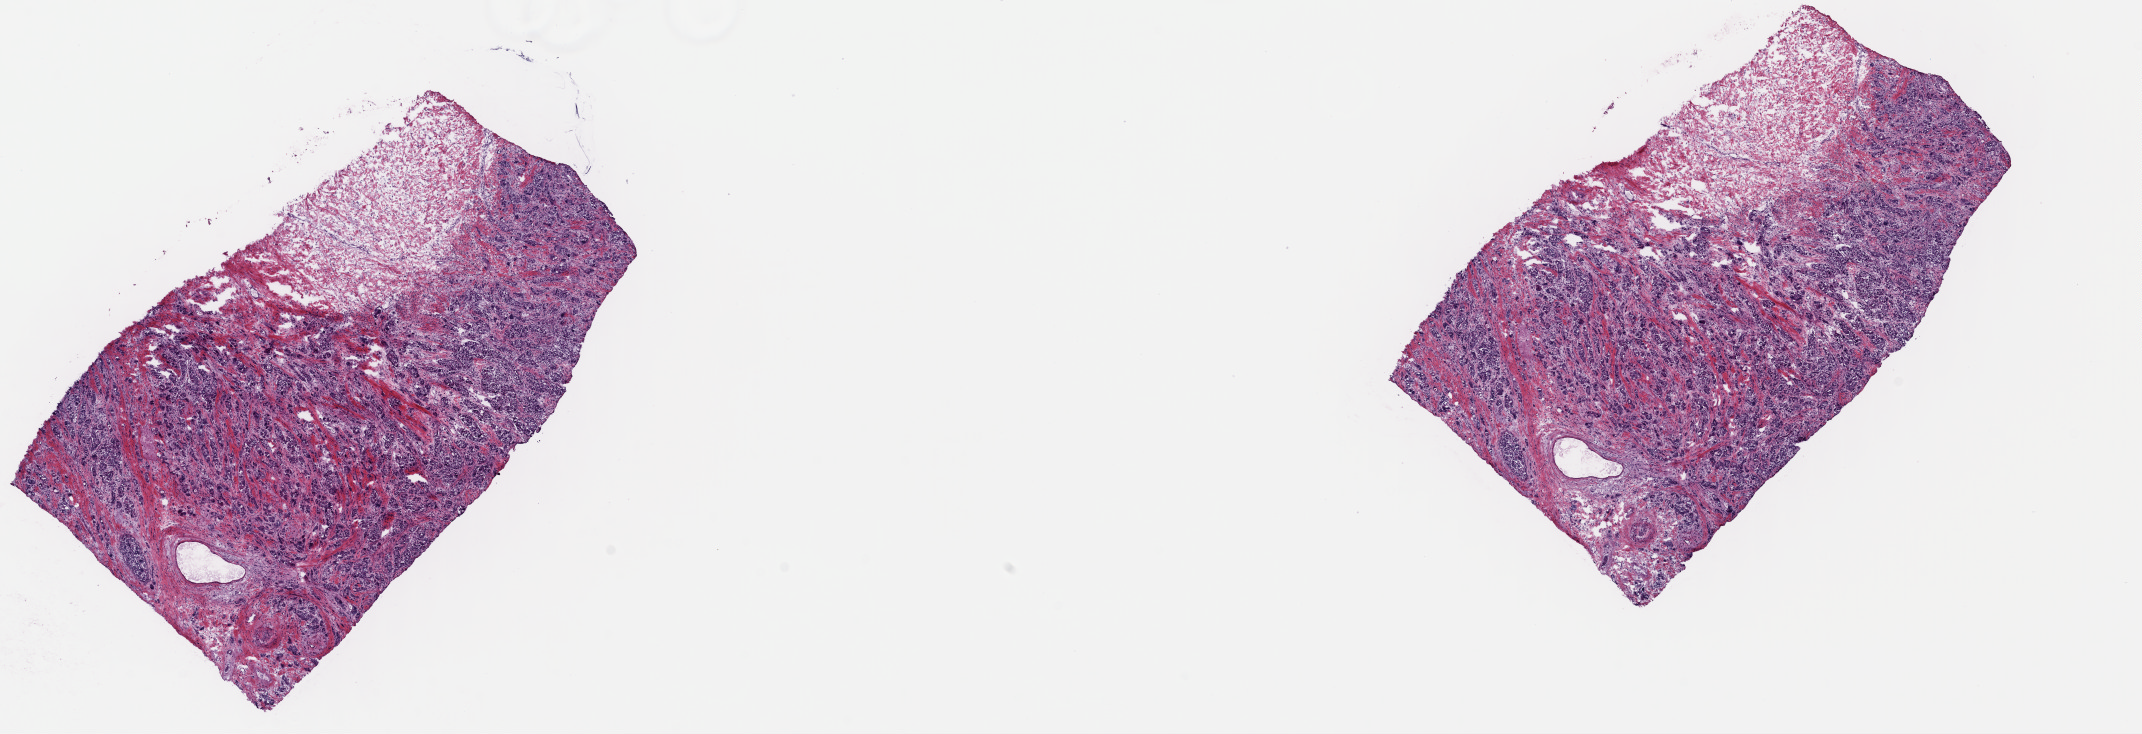
Whole-slide histology image, H&E-stained, whole scanned area (about 16.9 x 5.8 mm) shown as a low-resolution overview; frozen section from the top of the tissue portion; breast, primary tumour sample. Female patient; age at initial diagnosis 63 years. Pathologist review of this section (percent, as recorded): tumour cells 55%, tumour nuclei 85%, normal cells 0%, stromal cells 25%, necrosis 20%. Infiltration values recorded for this section: lymphocyte infiltration 1%, monocyte infiltration 0%, neutrophil infiltration 0%.
Lymph nodes positive (case pathology): 0 of 10 examined. Laterality: right. Pathologic diagnosis: Infiltrating duct carcinoma, NOS. AJCC pathologic stage: IIIB. TNM: T4b N0 MX.